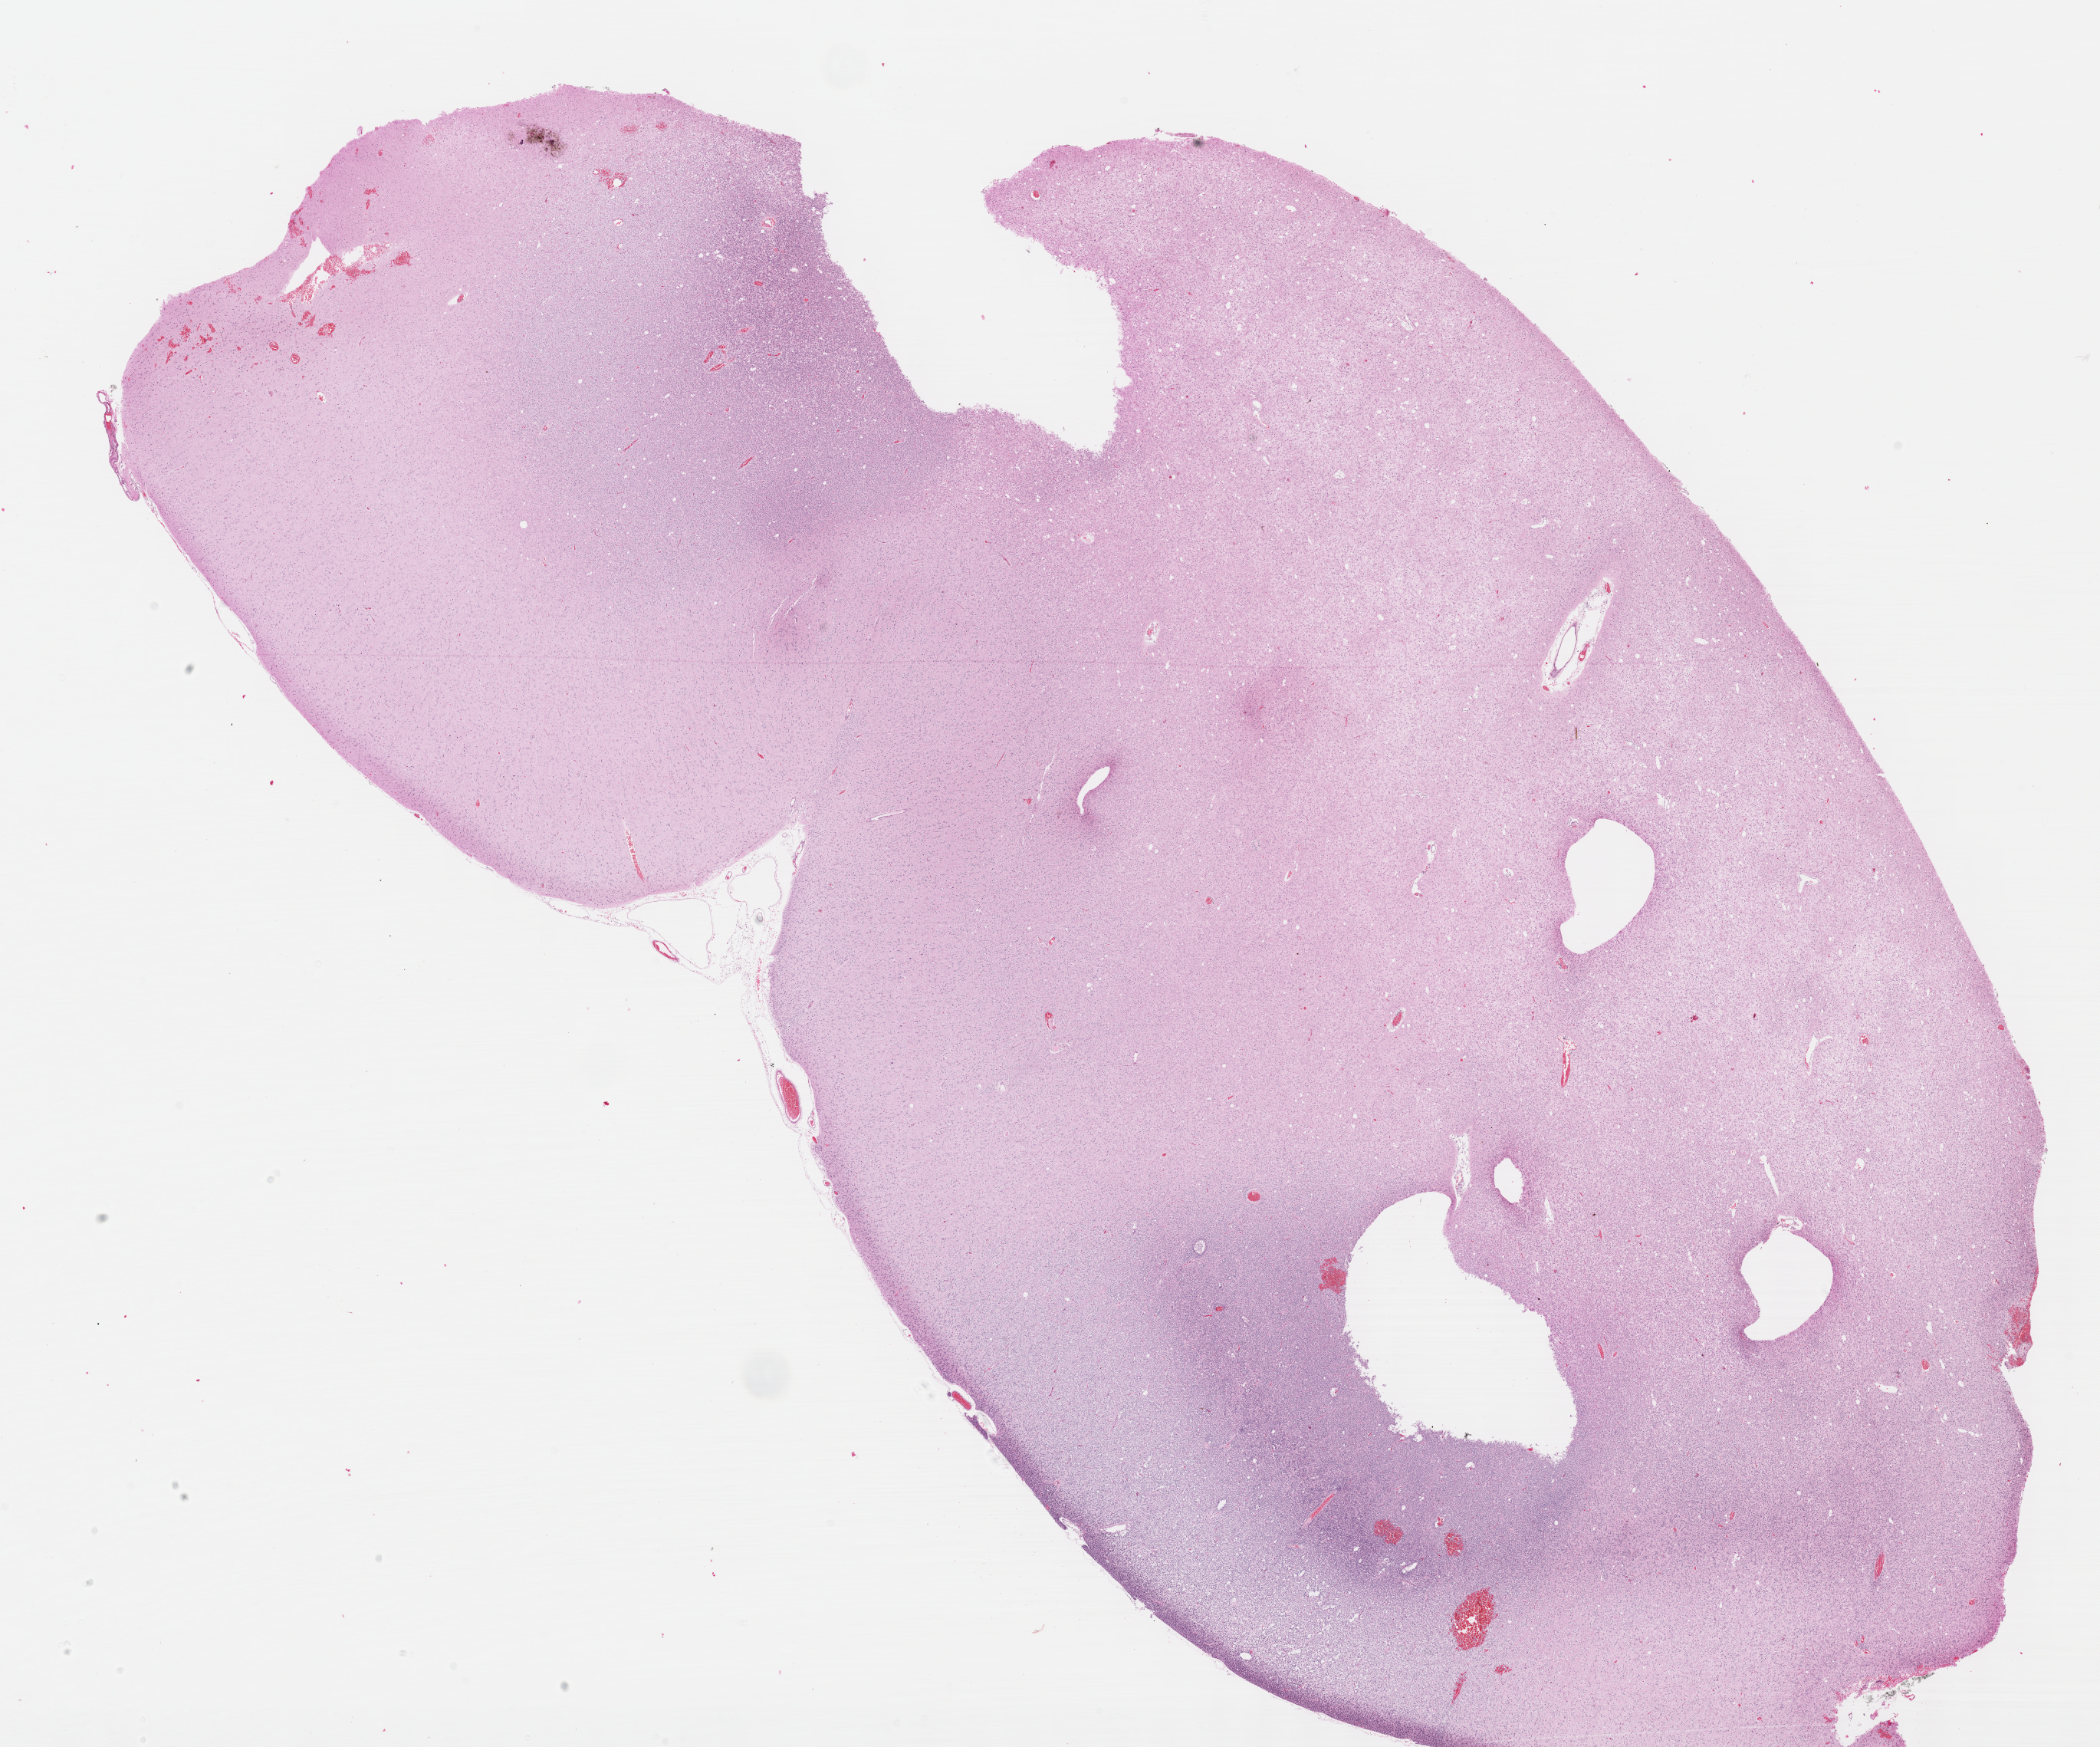
Digitized H&E tissue section (whole slide), a low-resolution overview of the entire scanned area, about 22.1 x 18.4 mm (acquisition: 40x scan), FFPE section, sample: primary tumour, brain. Female, age 37 years at initial diagnosis. Histologic grade: G2 (moderately differentiated).
Diagnosis: Oligodendroglioma, NOS.